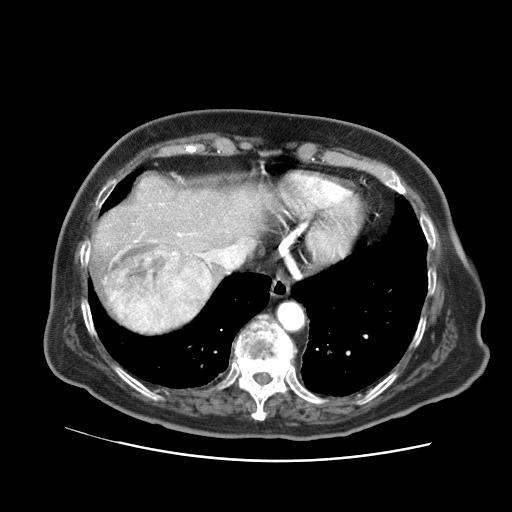
Contrast-enhanced abdominal CT (liver protocol), one axial slice; slice 58 of 73 in the series (ordered by position); reconstruction kernel STANDARD; 120 kVp; soft-tissue window (W 400 / L 40 HU); 2.5 mm slice thickness; 512 × 512 image matrix. Case-level facts recorded for this patient, not image findings: diagnosis: hepatocellular carcinoma (patient treated with transarterial chemoembolisation; whether this scan precedes or follows treatment is not stated here); TNM stage (as recorded): Stage-I; Child-Pugh class: A; tumour differentiation: well differentiated; tumour nodularity: uninodular.
Outlined on this slice (semi-automatic segmentation, software-assisted and operator-edited):
- abdominal aorta: box from (x=278, y=302) to (x=303, y=330) px
- liver parenchyma outside the tumour (the mass and vessels are separate outlines, so this box may not span the whole liver): (x=88, y=174)–(x=268, y=334)
- mass: (x=104, y=243)–(x=212, y=332)
- liver vessels: (x=135, y=204)–(x=218, y=279)